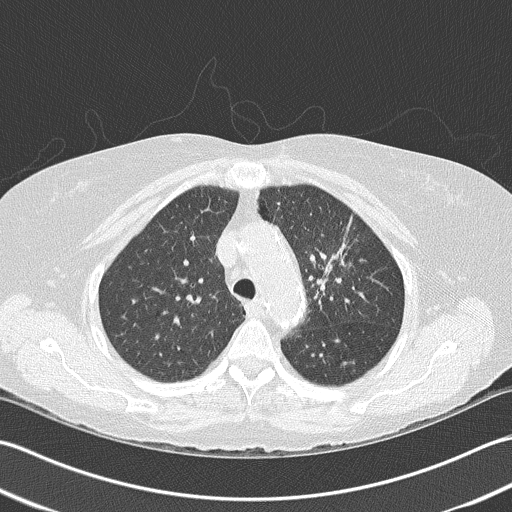
Axial slice from a low-dose chest CT screening exam, baseline annual screen, lung window (W 1500 / L -600 HU), 2 mm slice thickness, lung (sharp) reconstruction kernel (B50f), 512 × 512 image matrix. Female participant, aged 68 years at enrolment. Former smoker at enrolment.
Lesion marked by an expert reader, bounding box <297,215,372,303> (left, top, right, bottom; pixels). No non-calcified nodule or mass ≥4 mm was recorded by the screening reader at this exam. Later outcome: lung cancer diagnosed 763 days after this screen — adenocarcinoma, NOS, left upper lobe, poorly differentiated (G3), stage IB (AJCC 6th edition), 50 mm at pathology.